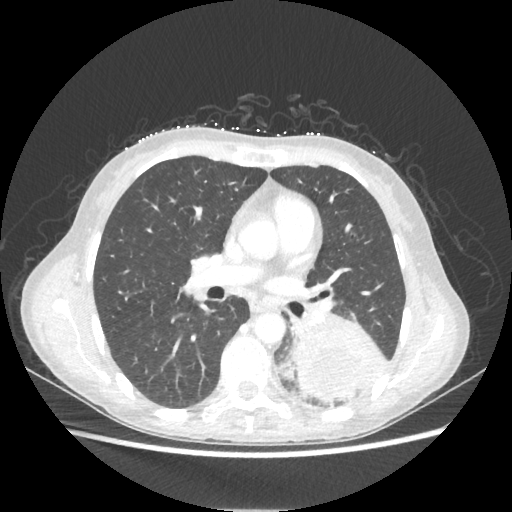
Chest CT, one axial slice; position 118 of 221 along the scan axis; reconstruction kernel STANDARD; 80 kVp; lung window (W 1500 / L -600 HU); 1.25 mm slice thickness; 512 × 512 image matrix. Patient: female, 53 years. Case-level facts recorded for this patient, not image findings: clinical TNM (as recorded): T3 N0 M0.
Structures marked on this image (rectangle marked by the reading radiologist):
- lung tumour (recorded histology: adenocarcinoma): box from (x=292, y=316) to (x=387, y=403) px